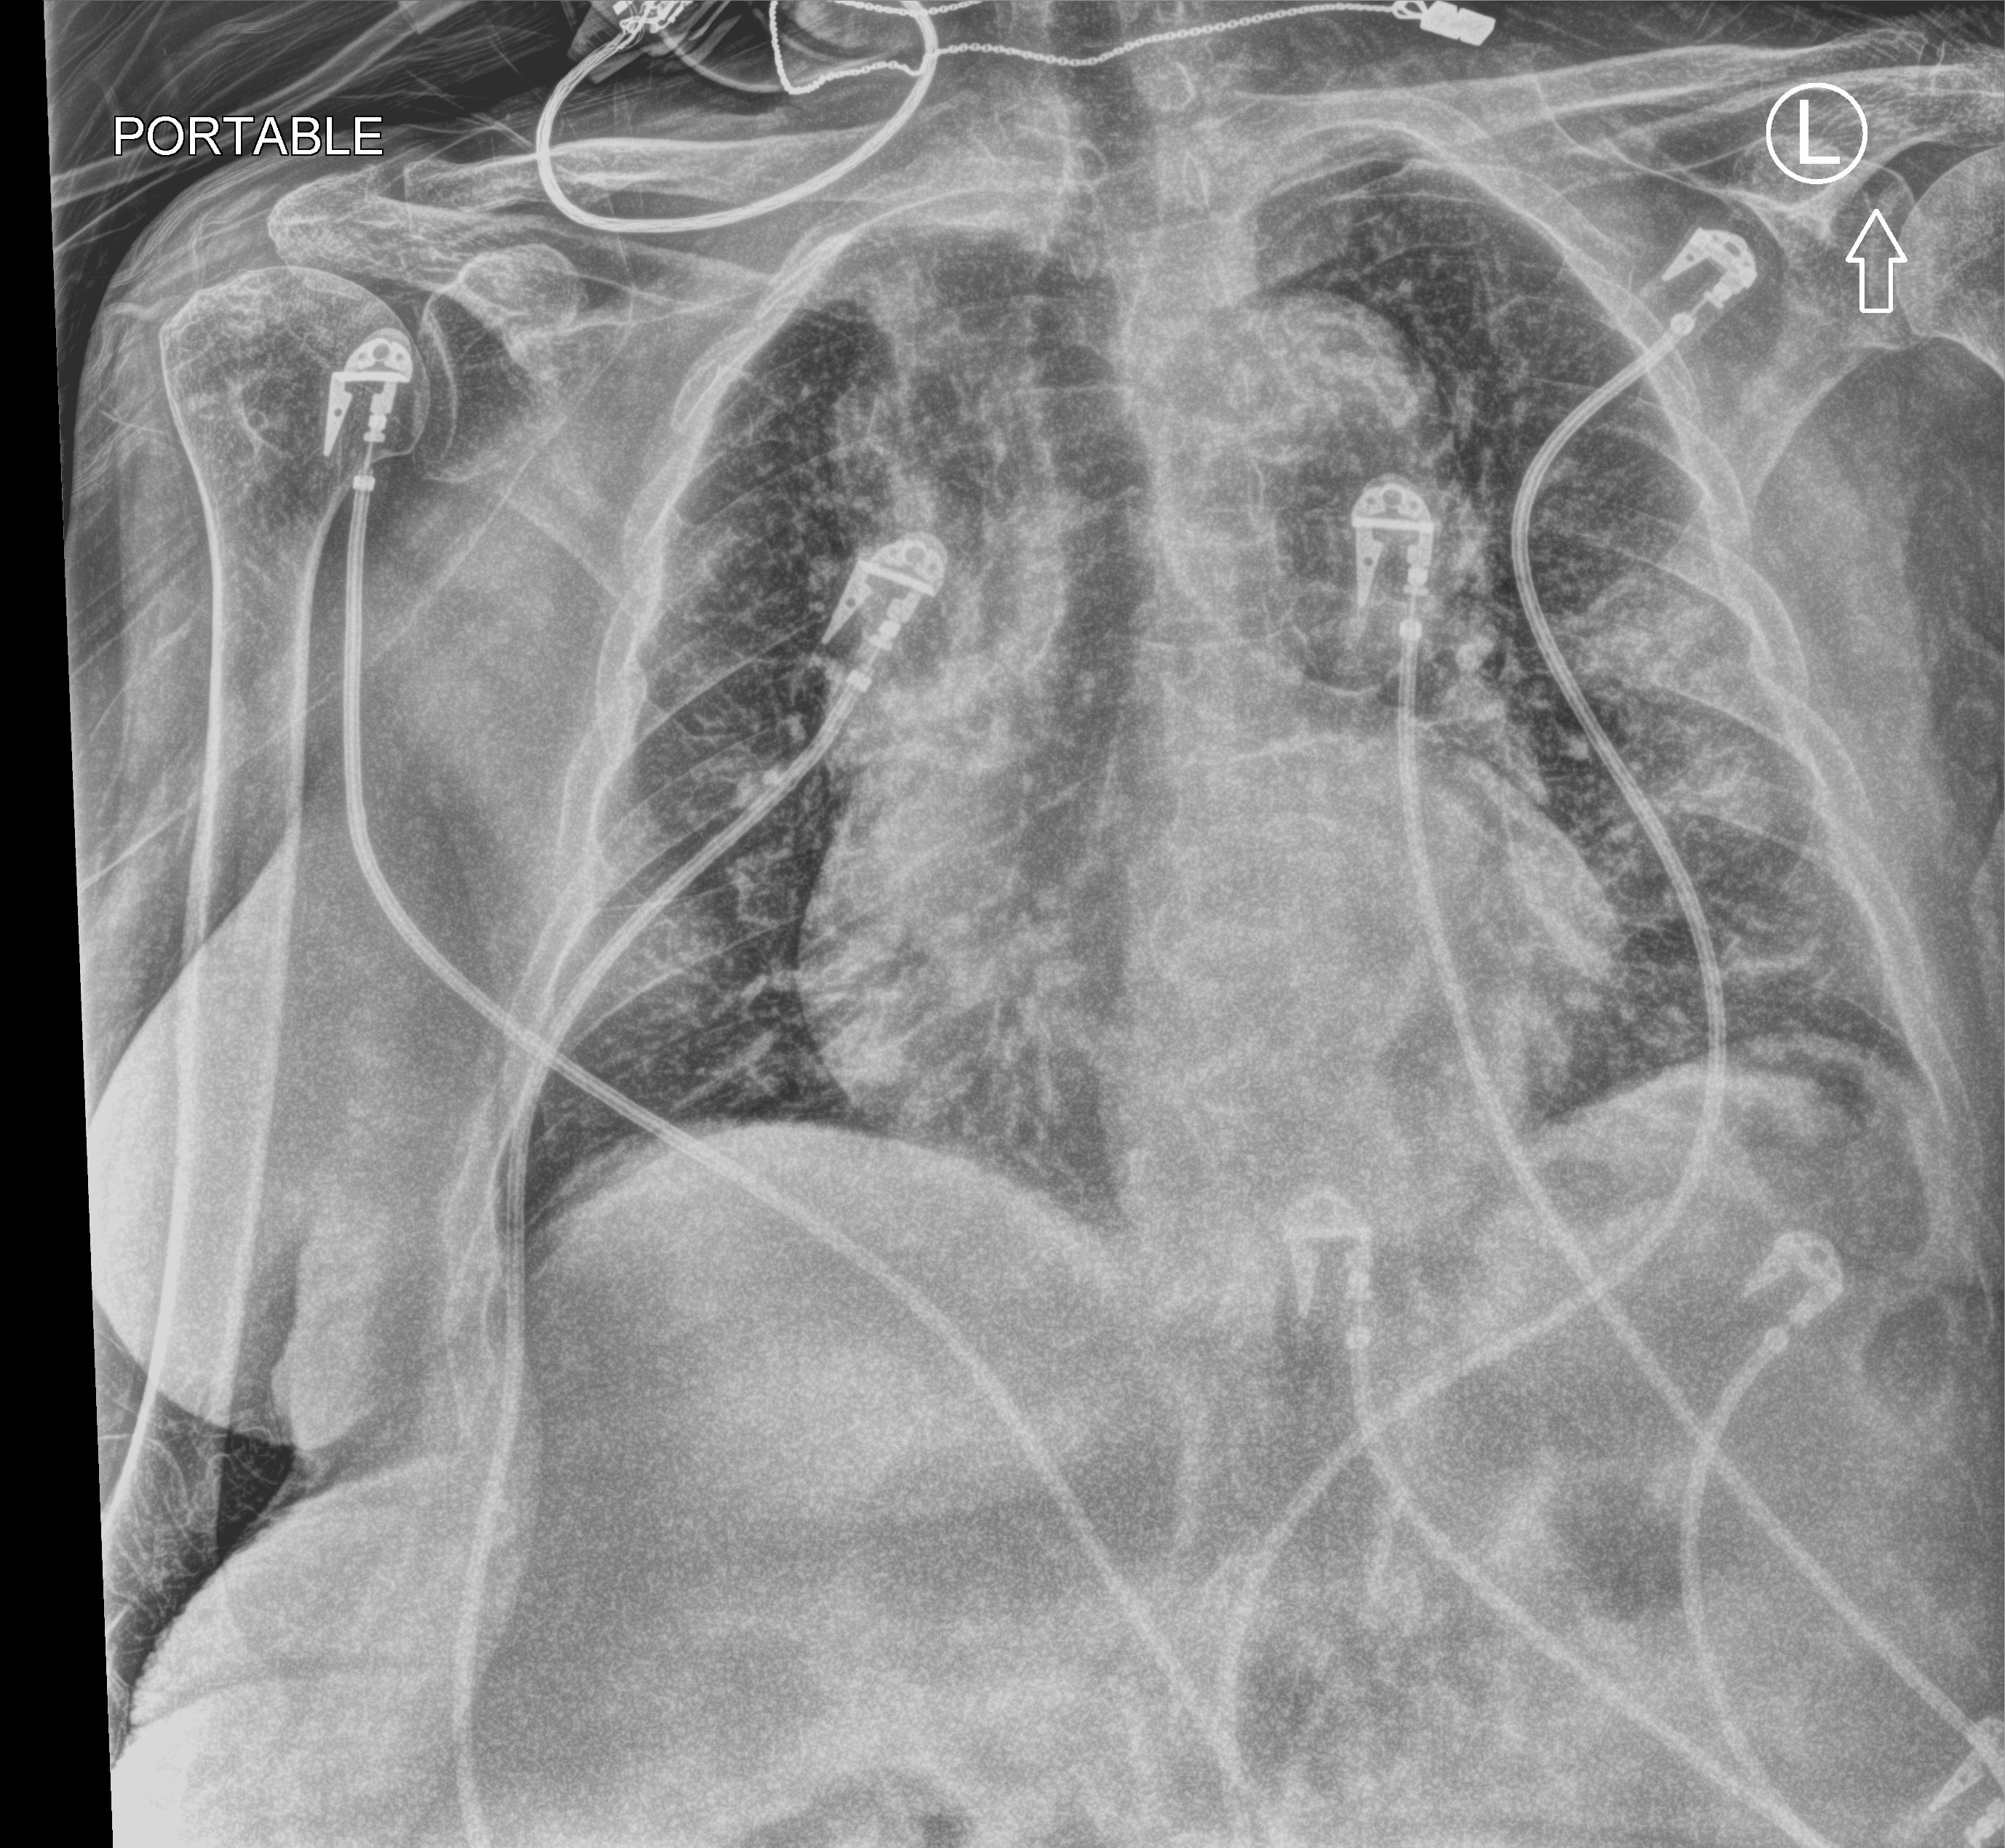
Portable chest radiograph, anteroposterior (AP) projection. Patient hospitalised with COVID-19; female, aged 75–90 years.
Admission-level facts for this patient (not findings on this image; timing relative to this image not recorded):
- length of hospital stay: 13 days